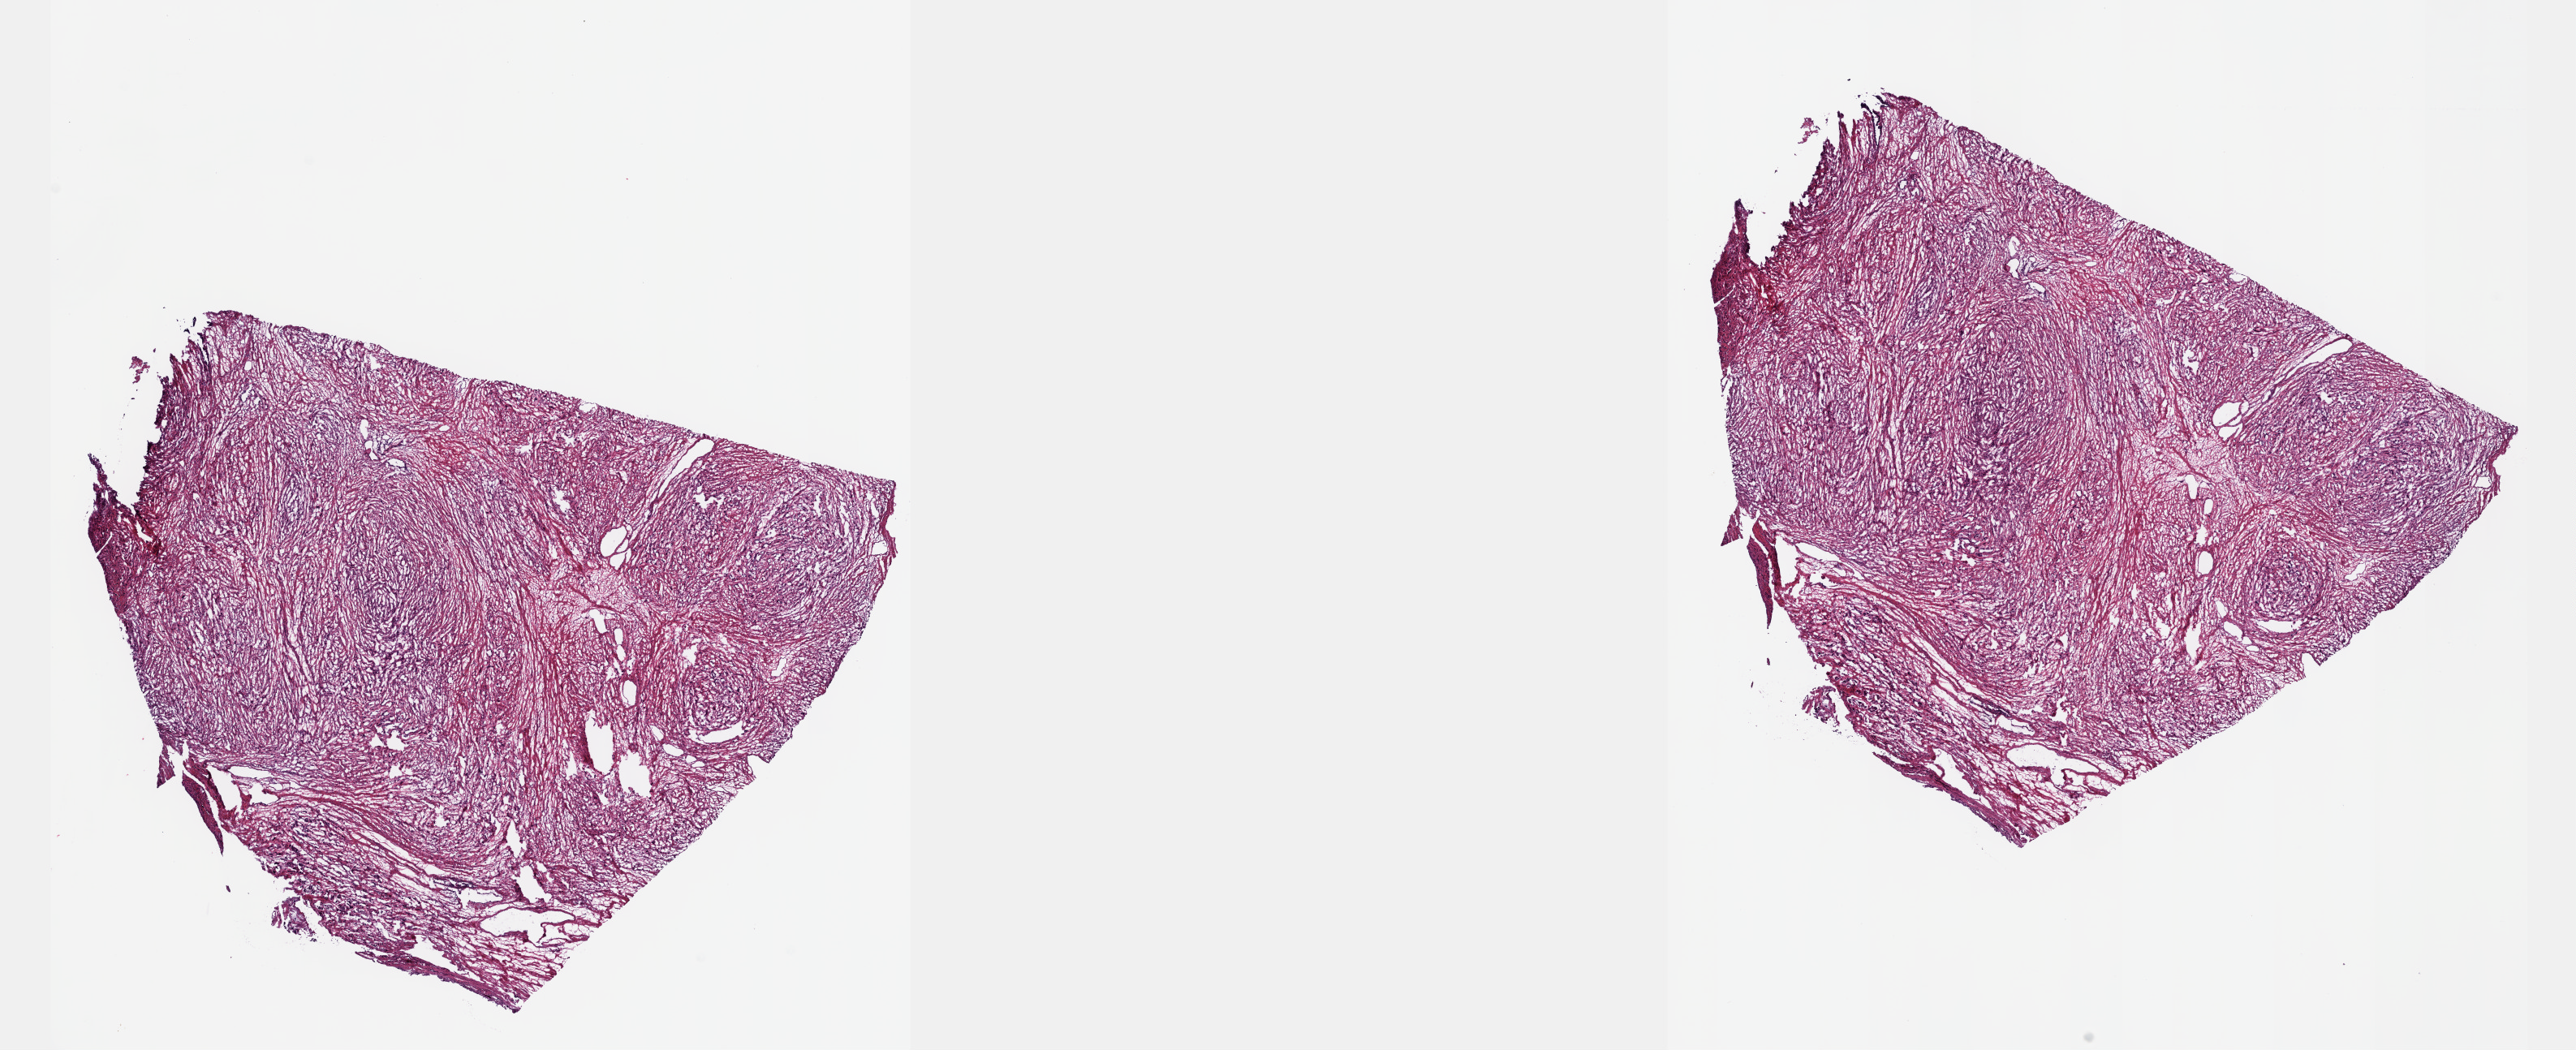
Digitized H&E tissue section (whole slide), shown as a low-resolution overview of the whole scanned area (about 25.7 x 10.5 mm); frozen section; primary tumour sample from the prostate. Patient: male, age at initial diagnosis 61 years. Gleason score: 9 (5+4). Pathologist review of this section (percent, as recorded): tumour cells 50%, tumour nuclei 60%, normal cells 0%, stromal cells 50%, necrosis 0%. Inflammatory infiltration, as recorded: lymphocyte infiltration 0%, monocyte infiltration 0%, neutrophil infiltration 0%.
Lymph nodes positive (case pathology): 0 of 10 examined. Diagnosis: Adenocarcinoma, NOS.